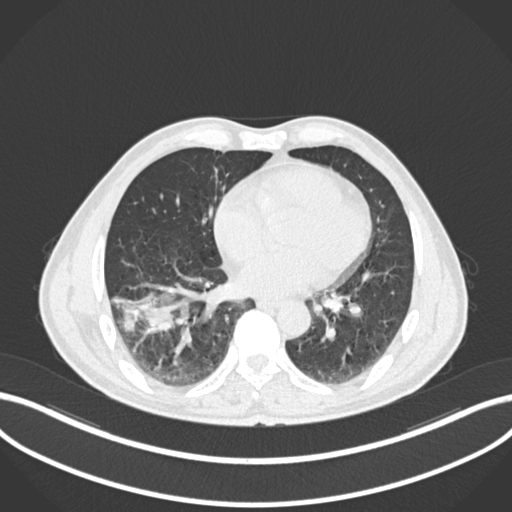
Chest CT, one axial slice; slice 70 of 208 in the series (ordered by position); 120 kVp; lung window (W 1500 / L -600 HU); 1 mm slice thickness; 512 × 512 image matrix, field of view 400 × 400 mm. Patient: male, 58 years. Case-level facts recorded for this patient, not image findings: clinical TNM (as recorded): T3 N0 M0; histopathological grade: G2.
Structures marked on this image (bounding box drawn by a radiologist):
- lung tumour (recorded histology: squamous cell carcinoma): bounding box [x1, y1, x2, y2] px = [116, 285, 184, 335]